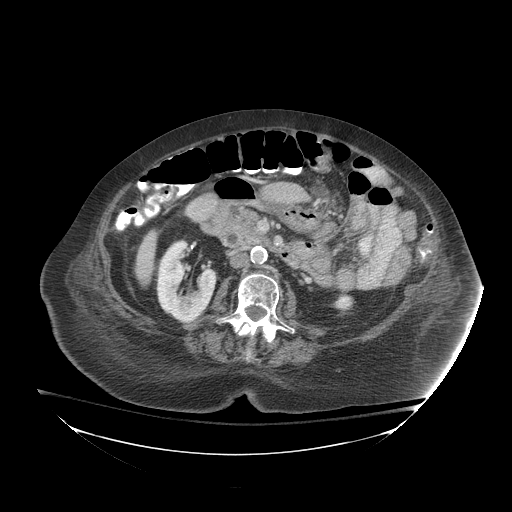
Contrast-enhanced abdominal CT (liver protocol), one axial slice. Position 22 of 81 along the scan axis. Reconstruction kernel STANDARD. 140 kVp. Soft-tissue window (W 400 / L 40 HU). 2.5 mm slice thickness. 512 × 512 image matrix, field of view 500 × 500 mm. From the clinical record (not read from this slice): diagnosis: hepatocellular carcinoma (patient treated with transarterial chemoembolisation; whether this scan precedes or follows treatment is not stated here); TNM stage (as recorded): Stage-I; Child-Pugh class: B.
Outlined on this slice (semi-automatically segmented with operator editing):
- liver parenchyma outside the tumour (the mass and vessels are separate outlines, so this box may not span the whole liver): box from (x=134, y=230) to (x=156, y=284) px